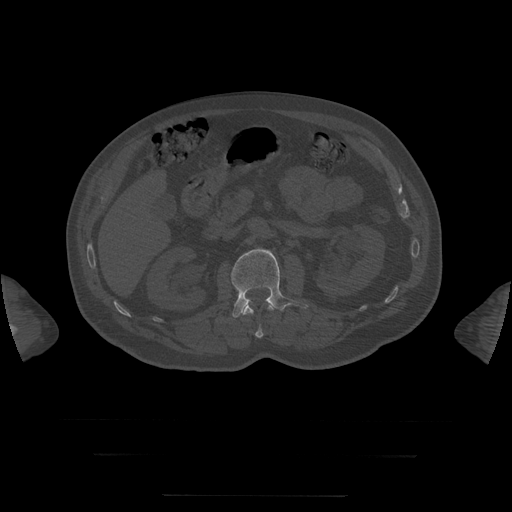
CT including the spine, one axial slice. Slice 30 of 397 in the series (ordered by position). Bone window (W 1800 / L 400 HU). 1.25 mm slice thickness. 512 × 512 image matrix. Patient age 73 years. Case-level facts recorded for this patient, not image findings: primary cancer: prostate.
Structures marked on this image (semi-automatically segmented with operator editing):
- L1 vertebra: bounding box [x1, y1, x2, y2] px = [243, 302, 274, 339]